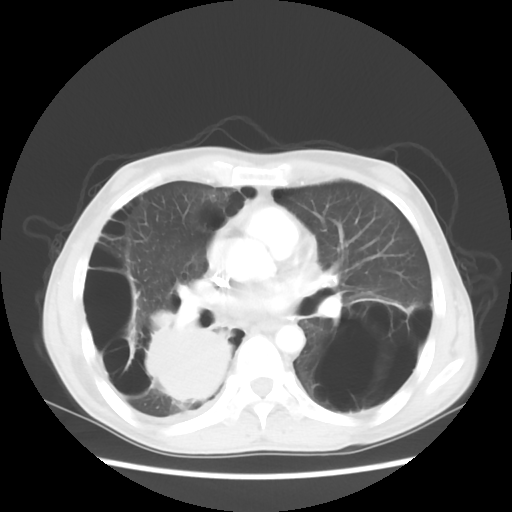
Chest CT, one axial slice. Position 28 of 56 along the scan axis. Reconstruction kernel STANDARD. Lung window (W 1500 / L -600 HU). 5 mm slice thickness. 512 × 512 image matrix, field of view 351 × 351 mm. Male patient, age 41 years. From the clinical record (not read from this slice): clinical TNM (as recorded): T4 N0 M1a.
Annotated regions visible in this slice (bounding box drawn by a radiologist):
- lung tumour (recorded histology: large cell carcinoma): box from (x=128, y=298) to (x=259, y=432) px